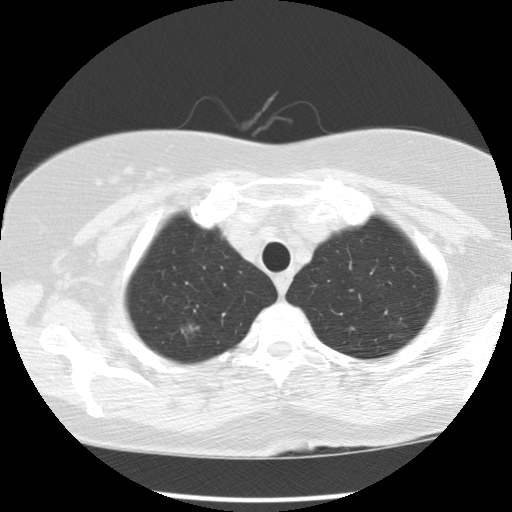
Low-dose screening chest CT, one axial slice. Slice 108 of 122 in the series (ordered by position). Reconstruction kernel STANDARD. 120 kVp. Lung window (W 1500 / L -600 HU). 2.5 mm slice thickness. 512 × 512 image matrix, field of view 329 × 329 mm.
Outlined on this slice (outlined manually by an expert reader):
- lesion 1 (tumor, upper lobe of right lung): box from (x=181, y=321) to (x=200, y=339) px